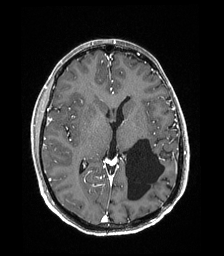
Brain MRI from a brain-tumour surgery series, one axial slice. Slice 95 of 192 in the series (ordered by position). T1-weighted post-contrast. 224 × 256 image matrix, field of view 224 × 256 mm. From the clinical record (not read from this slice): histopathology: Low grade glioma; IDH mutation: no; tumour location: Left Parieto-Occipital Intraventricular.
Outlined on this slice (outlined manually by an expert reader):
- previous resection cavity: box from (x=125, y=138) to (x=164, y=201) px